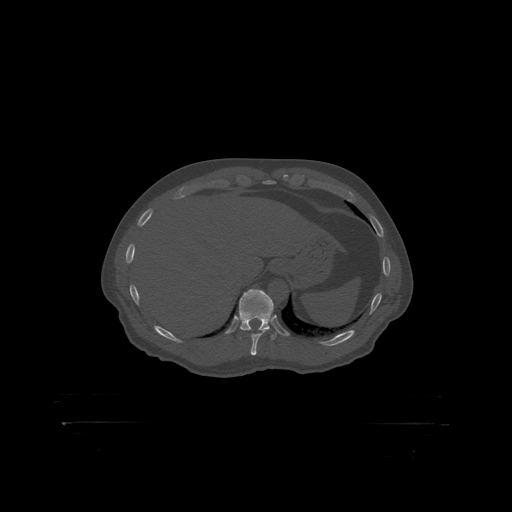
CT including the spine, one axial slice; slice 389 of 399 in the series (ordered by position); reconstruction kernel STANDARD; 120 kVp; bone window (W 1800 / L 400 HU); 1.25 mm slice thickness; 512 × 512 image matrix, field of view 650 × 650 mm. Male patient, age 46 years. From the clinical record (not read from this slice): primary cancer: skin.
Outlined on this slice (semi-automatic segmentation, software-assisted and operator-edited):
- T11 vertebra: bounding box [x1, y1, x2, y2] px = [240, 290, 274, 319]